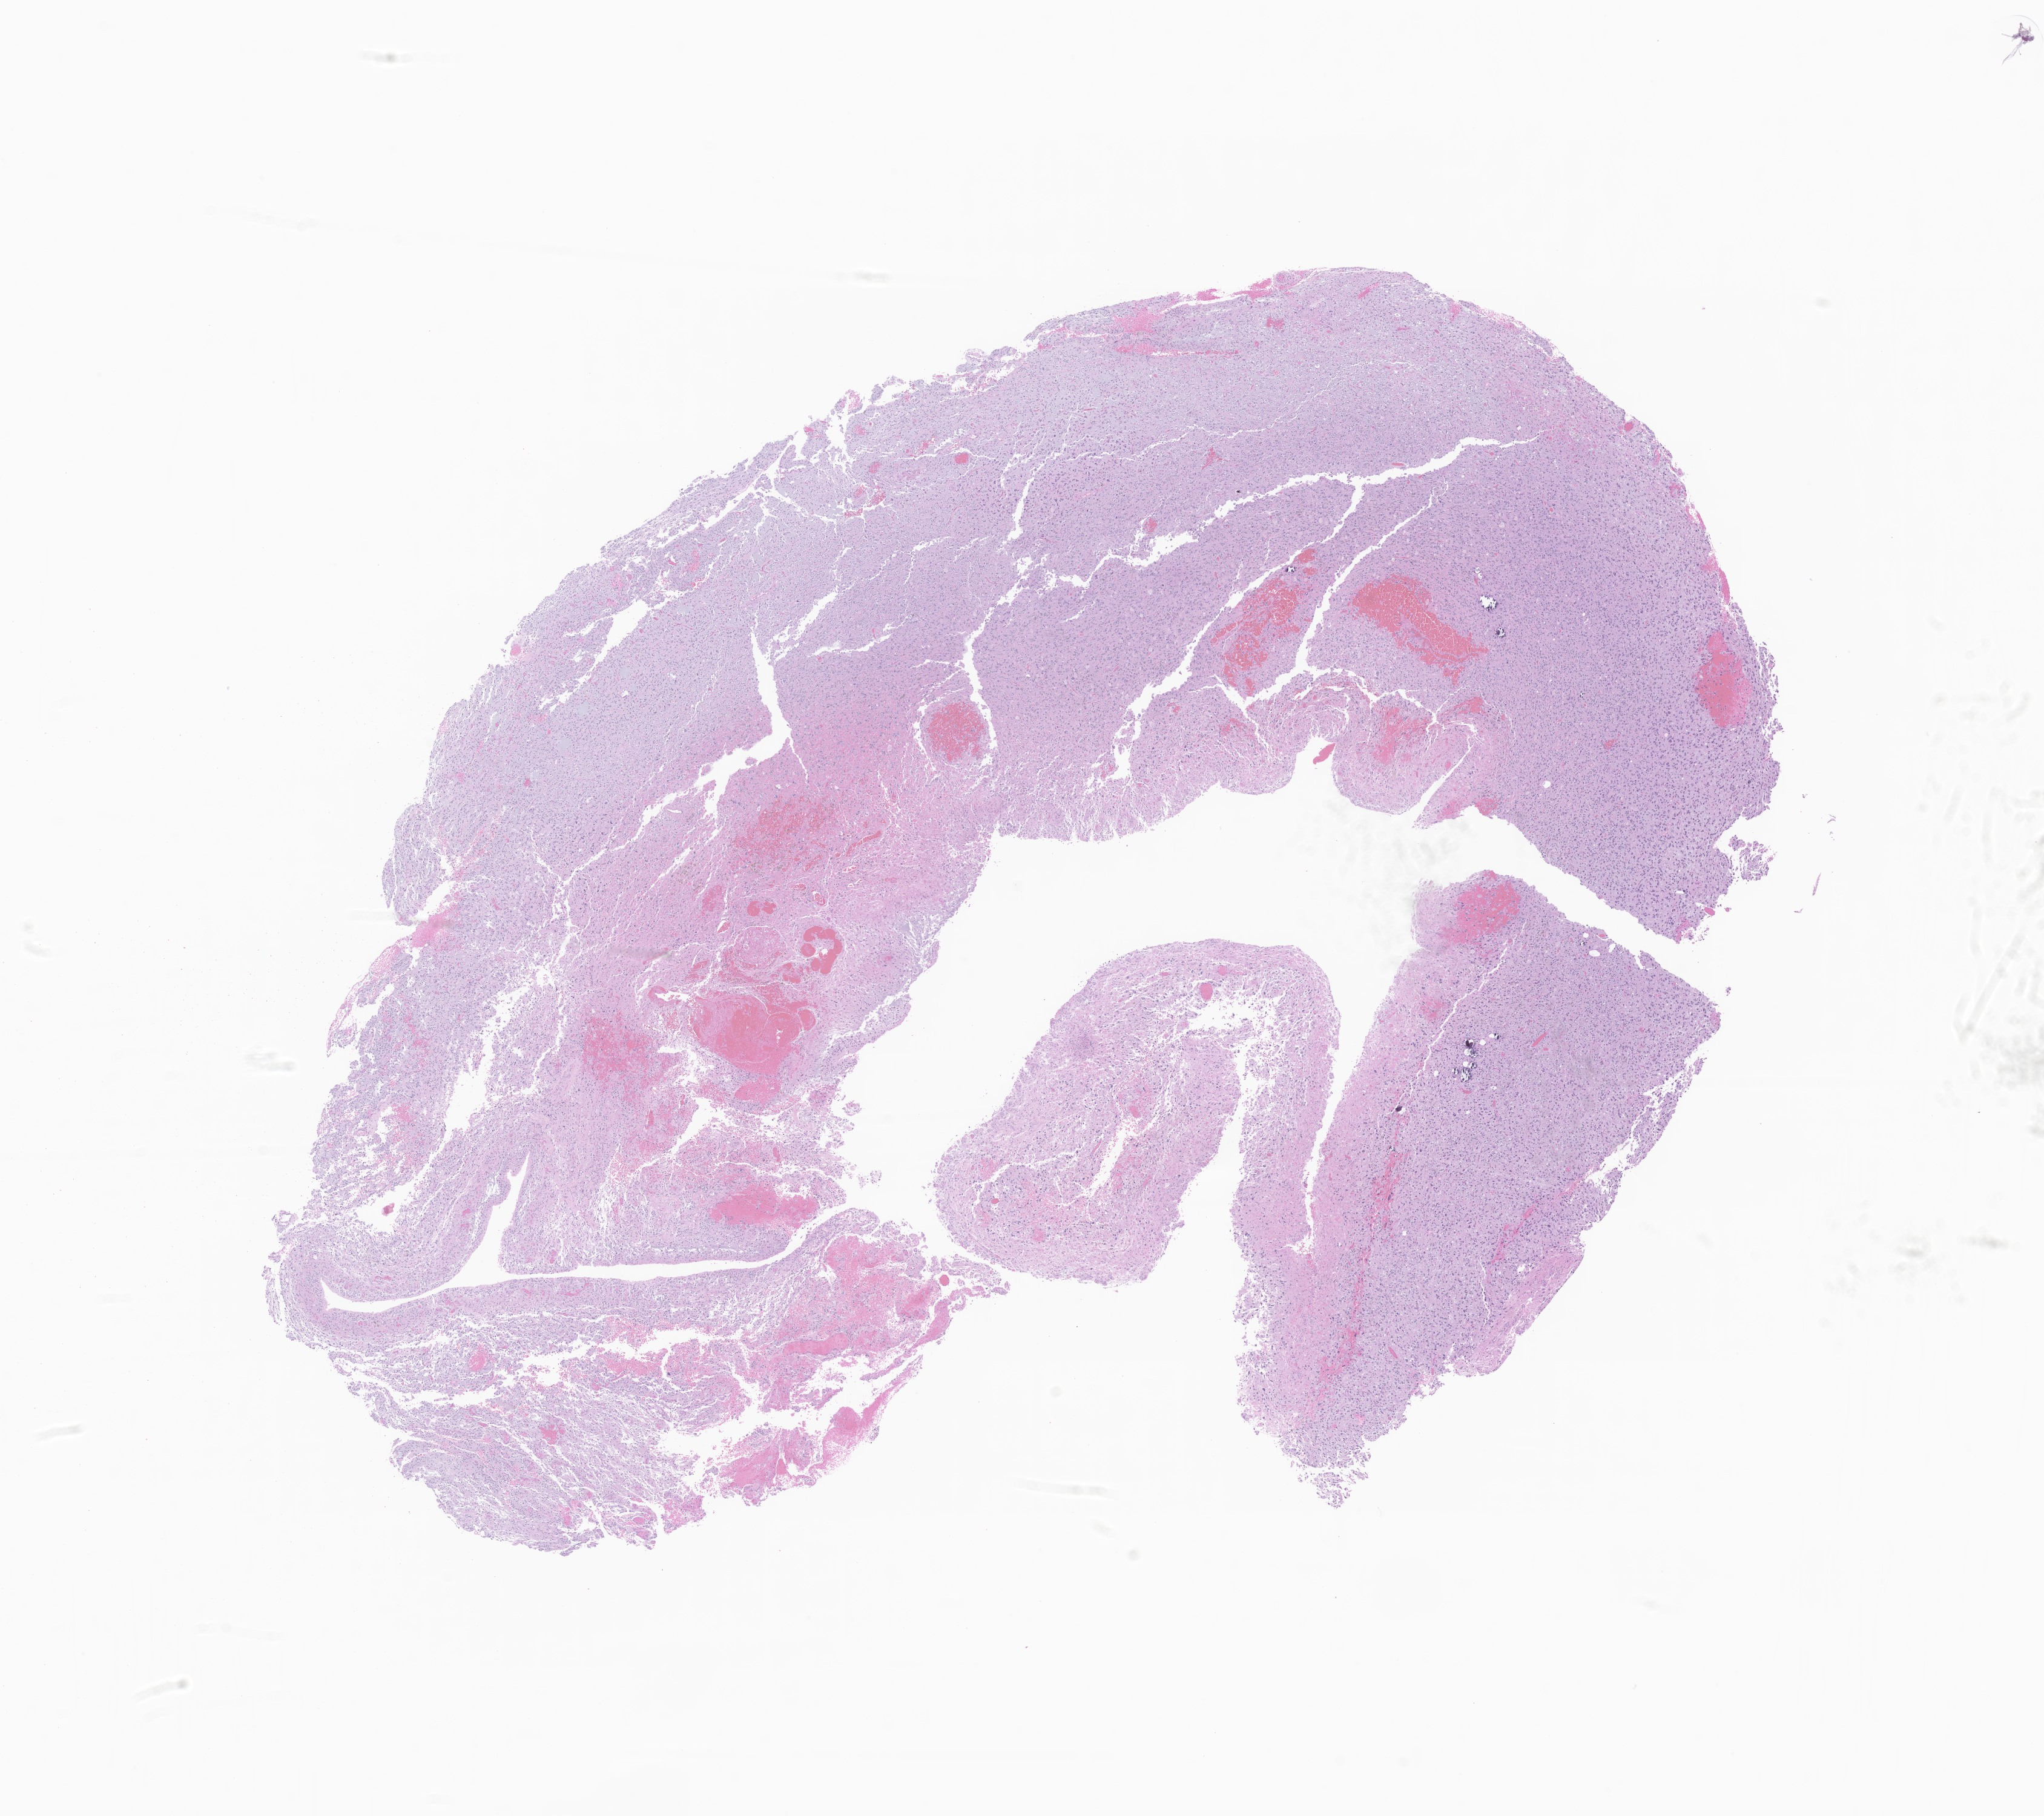
Whole-slide image, H&E stain of tumor tissue from the brain, whole scanned area (about 14.2 x 12.6 mm) shown as a low-resolution overview; FFPE section. Patient male; age 249 months (20 years 9 months).
* diagnosis (ICD-O-3 morphology term): Ganglioglioma, NOS